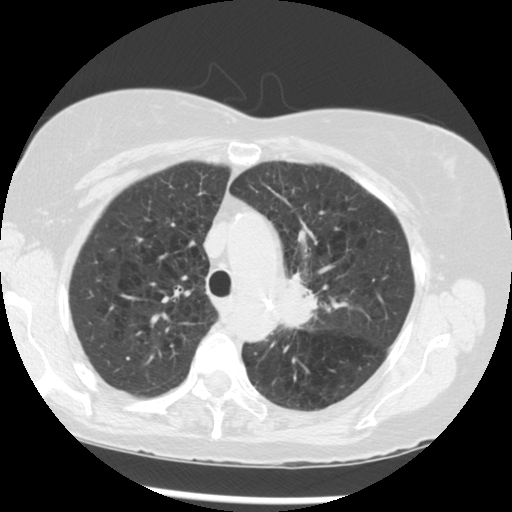
Low-dose screening chest CT, one axial slice. Slice 210 of 283 in the series (ordered by position). 120 kVp. Lung window (W 1500 / L -600 HU). 512 × 512 image matrix, field of view 330 × 330 mm.
Annotated regions visible in this slice (expert manual segmentation):
- lesion 1 (tumor, upper lobe of left lung): bounding box (x1, y1, x2, y2) in pixels: (280, 274, 318, 328)